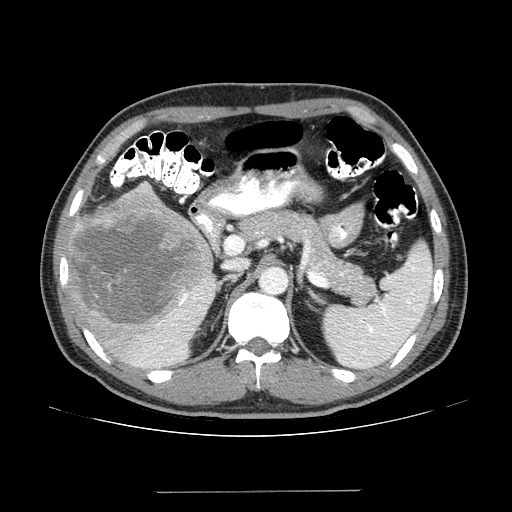
Contrast-enhanced abdominal CT (liver protocol), one axial slice; position 81 of 131 along the scan axis; reconstruction kernel STANDARD; one of 2 acquisitions stored at this slice position; soft-tissue window (W 400 / L 40 HU); 512 × 512 image matrix, field of view 380 × 380 mm. Case-level facts recorded for this patient, not image findings: diagnosis: hepatocellular carcinoma (patient treated with transarterial chemoembolisation; whether this scan precedes or follows treatment is not stated here); TNM stage (as recorded): Stage-I; Child-Pugh class: A; tumour differentiation: poorly differentiated; tumour nodularity: uninodular.
Structures marked on this image (semi-automatically segmented with operator editing):
- liver parenchyma outside the tumour (the mass and vessels are separate outlines, so this box may not span the whole liver): bounding box (x1, y1, x2, y2) in pixels: (66, 182, 218, 368)
- mass: (67, 187, 211, 332)
- liver vessels: (139, 296, 205, 362)